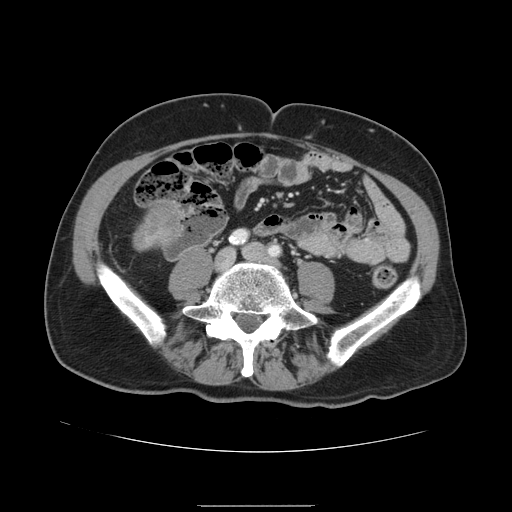
Contrast-enhanced abdominal CT, one axial slice. Position 7 of 168 along the scan axis. 120 kVp. Intravenous contrast given. Soft-tissue window (W 400 / L 40 HU). 512 × 512 image matrix, field of view 386 × 386 mm. Male patient, age 74 years. Case-level facts recorded for this patient, not image findings: diagnosis: colorectal cancer liver metastases, imaged before liver resection; multiple liver metastases: no.
Structures marked on this image (expert manual segmentation):
- liver: box from (x=133, y=199) to (x=187, y=250) px
- liver metastasis: (x=137, y=204)–(x=181, y=244)